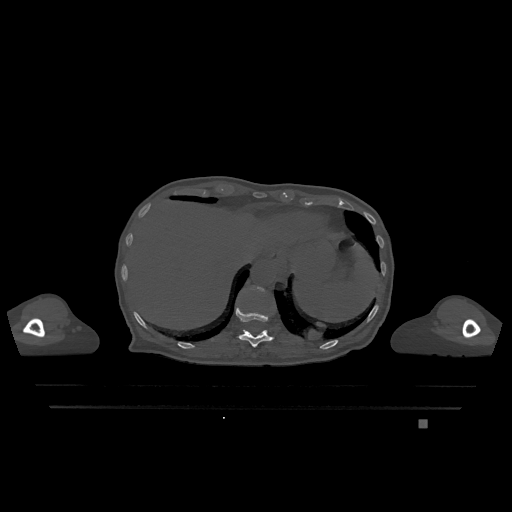
CT including the spine, one axial slice. Position 578 of 1317 along the scan axis. Bone window (W 1800 / L 400 HU). 0.5 mm slice thickness. 512 × 512 image matrix, field of view 500 × 500 mm. Patient: female, 74 years. Case-level facts recorded for this patient, not image findings: primary cancer: lung.
Structures marked on this image (semi-automatically segmented with operator editing):
- T11 vertebra: bounding box [x1, y1, x2, y2] px = [236, 305, 274, 348]
- T12 vertebra: [257, 287, 265, 291]